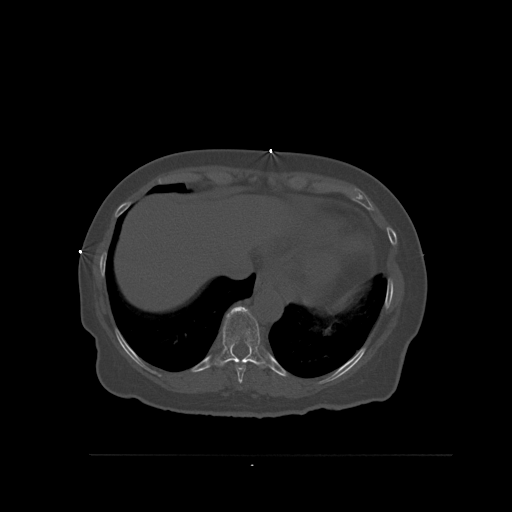
CT including the spine, one axial slice. Slice 323 of 527 in the series (ordered by position). Bone window (W 1800 / L 400 HU). 512 × 512 image matrix, field of view 470 × 470 mm. Female patient, age 73 years. From the clinical record (not read from this slice): primary cancer: breast; vertebrae with lytic lesions (as recorded): L2.
Structures marked on this image (semi-automatically segmented with operator editing):
- T10 vertebra: bounding box [x1, y1, x2, y2] px = [212, 306, 269, 368]
- T9 vertebra: [235, 363, 246, 384]